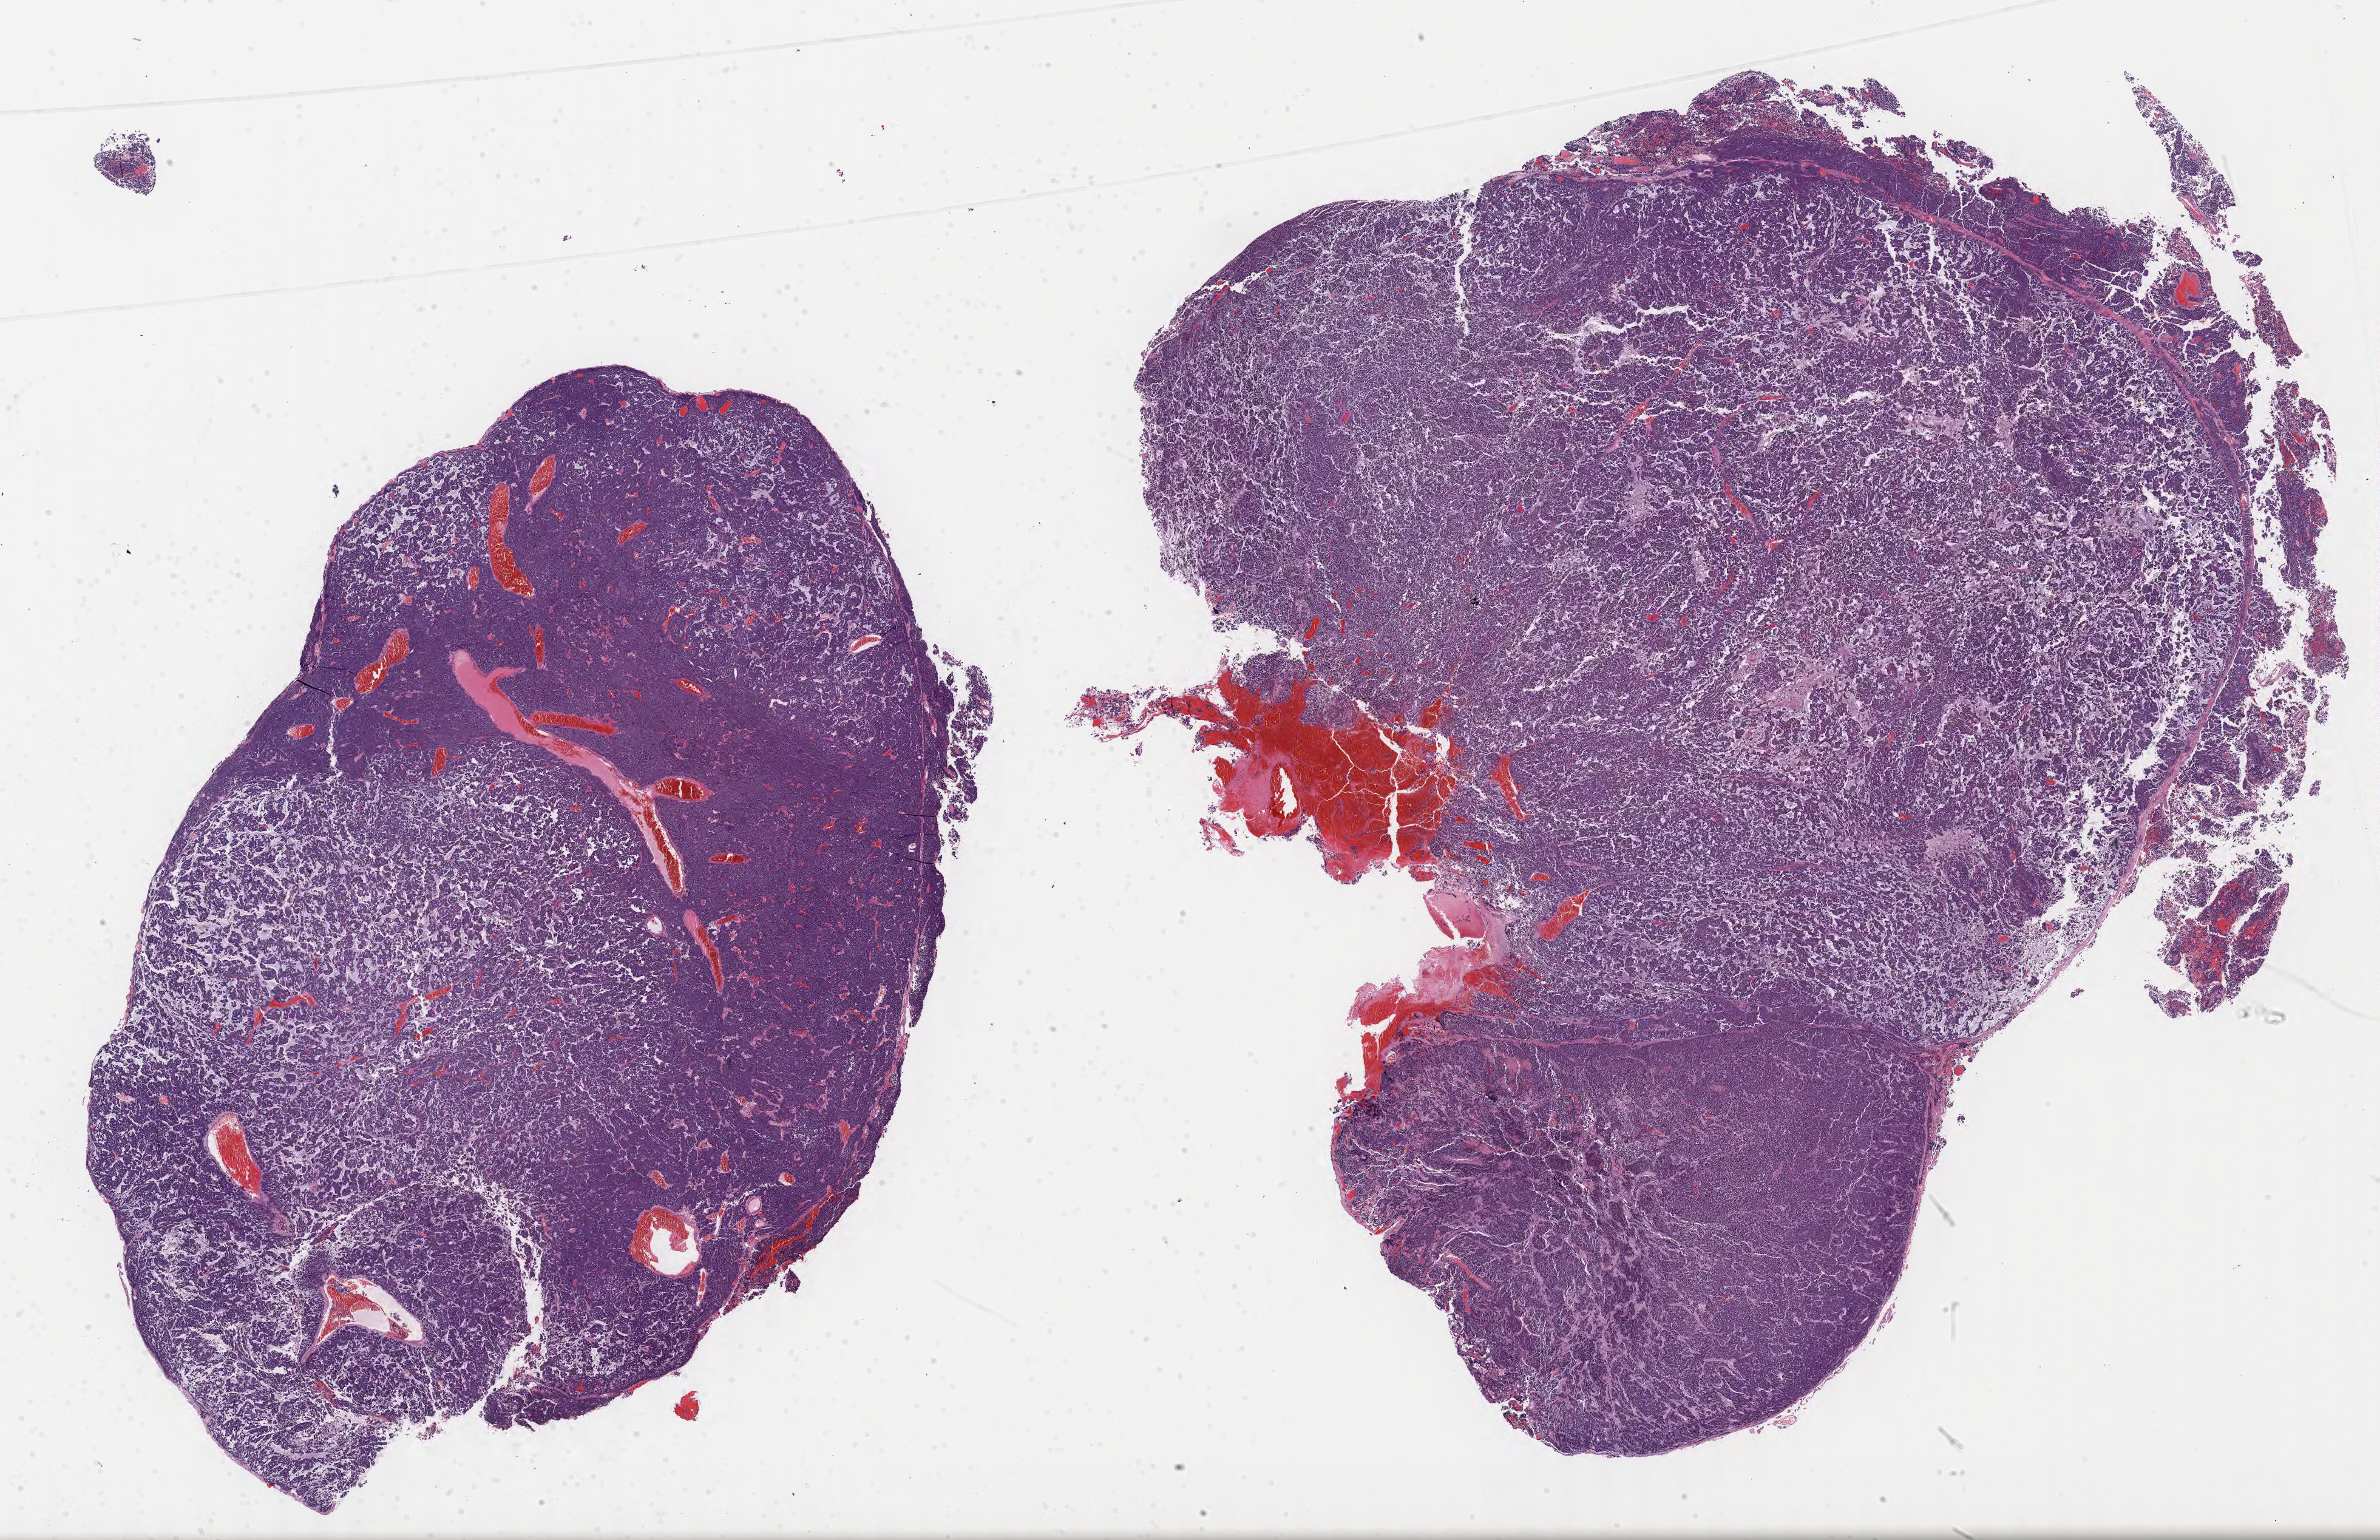
Hematoxylin and eosin (H&E) whole-slide image of tumor tissue from the cerebral ventricle, whole scanned area (about 31.7 x 20.5 mm) shown as a low-resolution overview. FFPE section. Patient male; age 248 months (20 years 8 months).
* recorded diagnosis: Neoplasm, uncertain whether benign or malignant